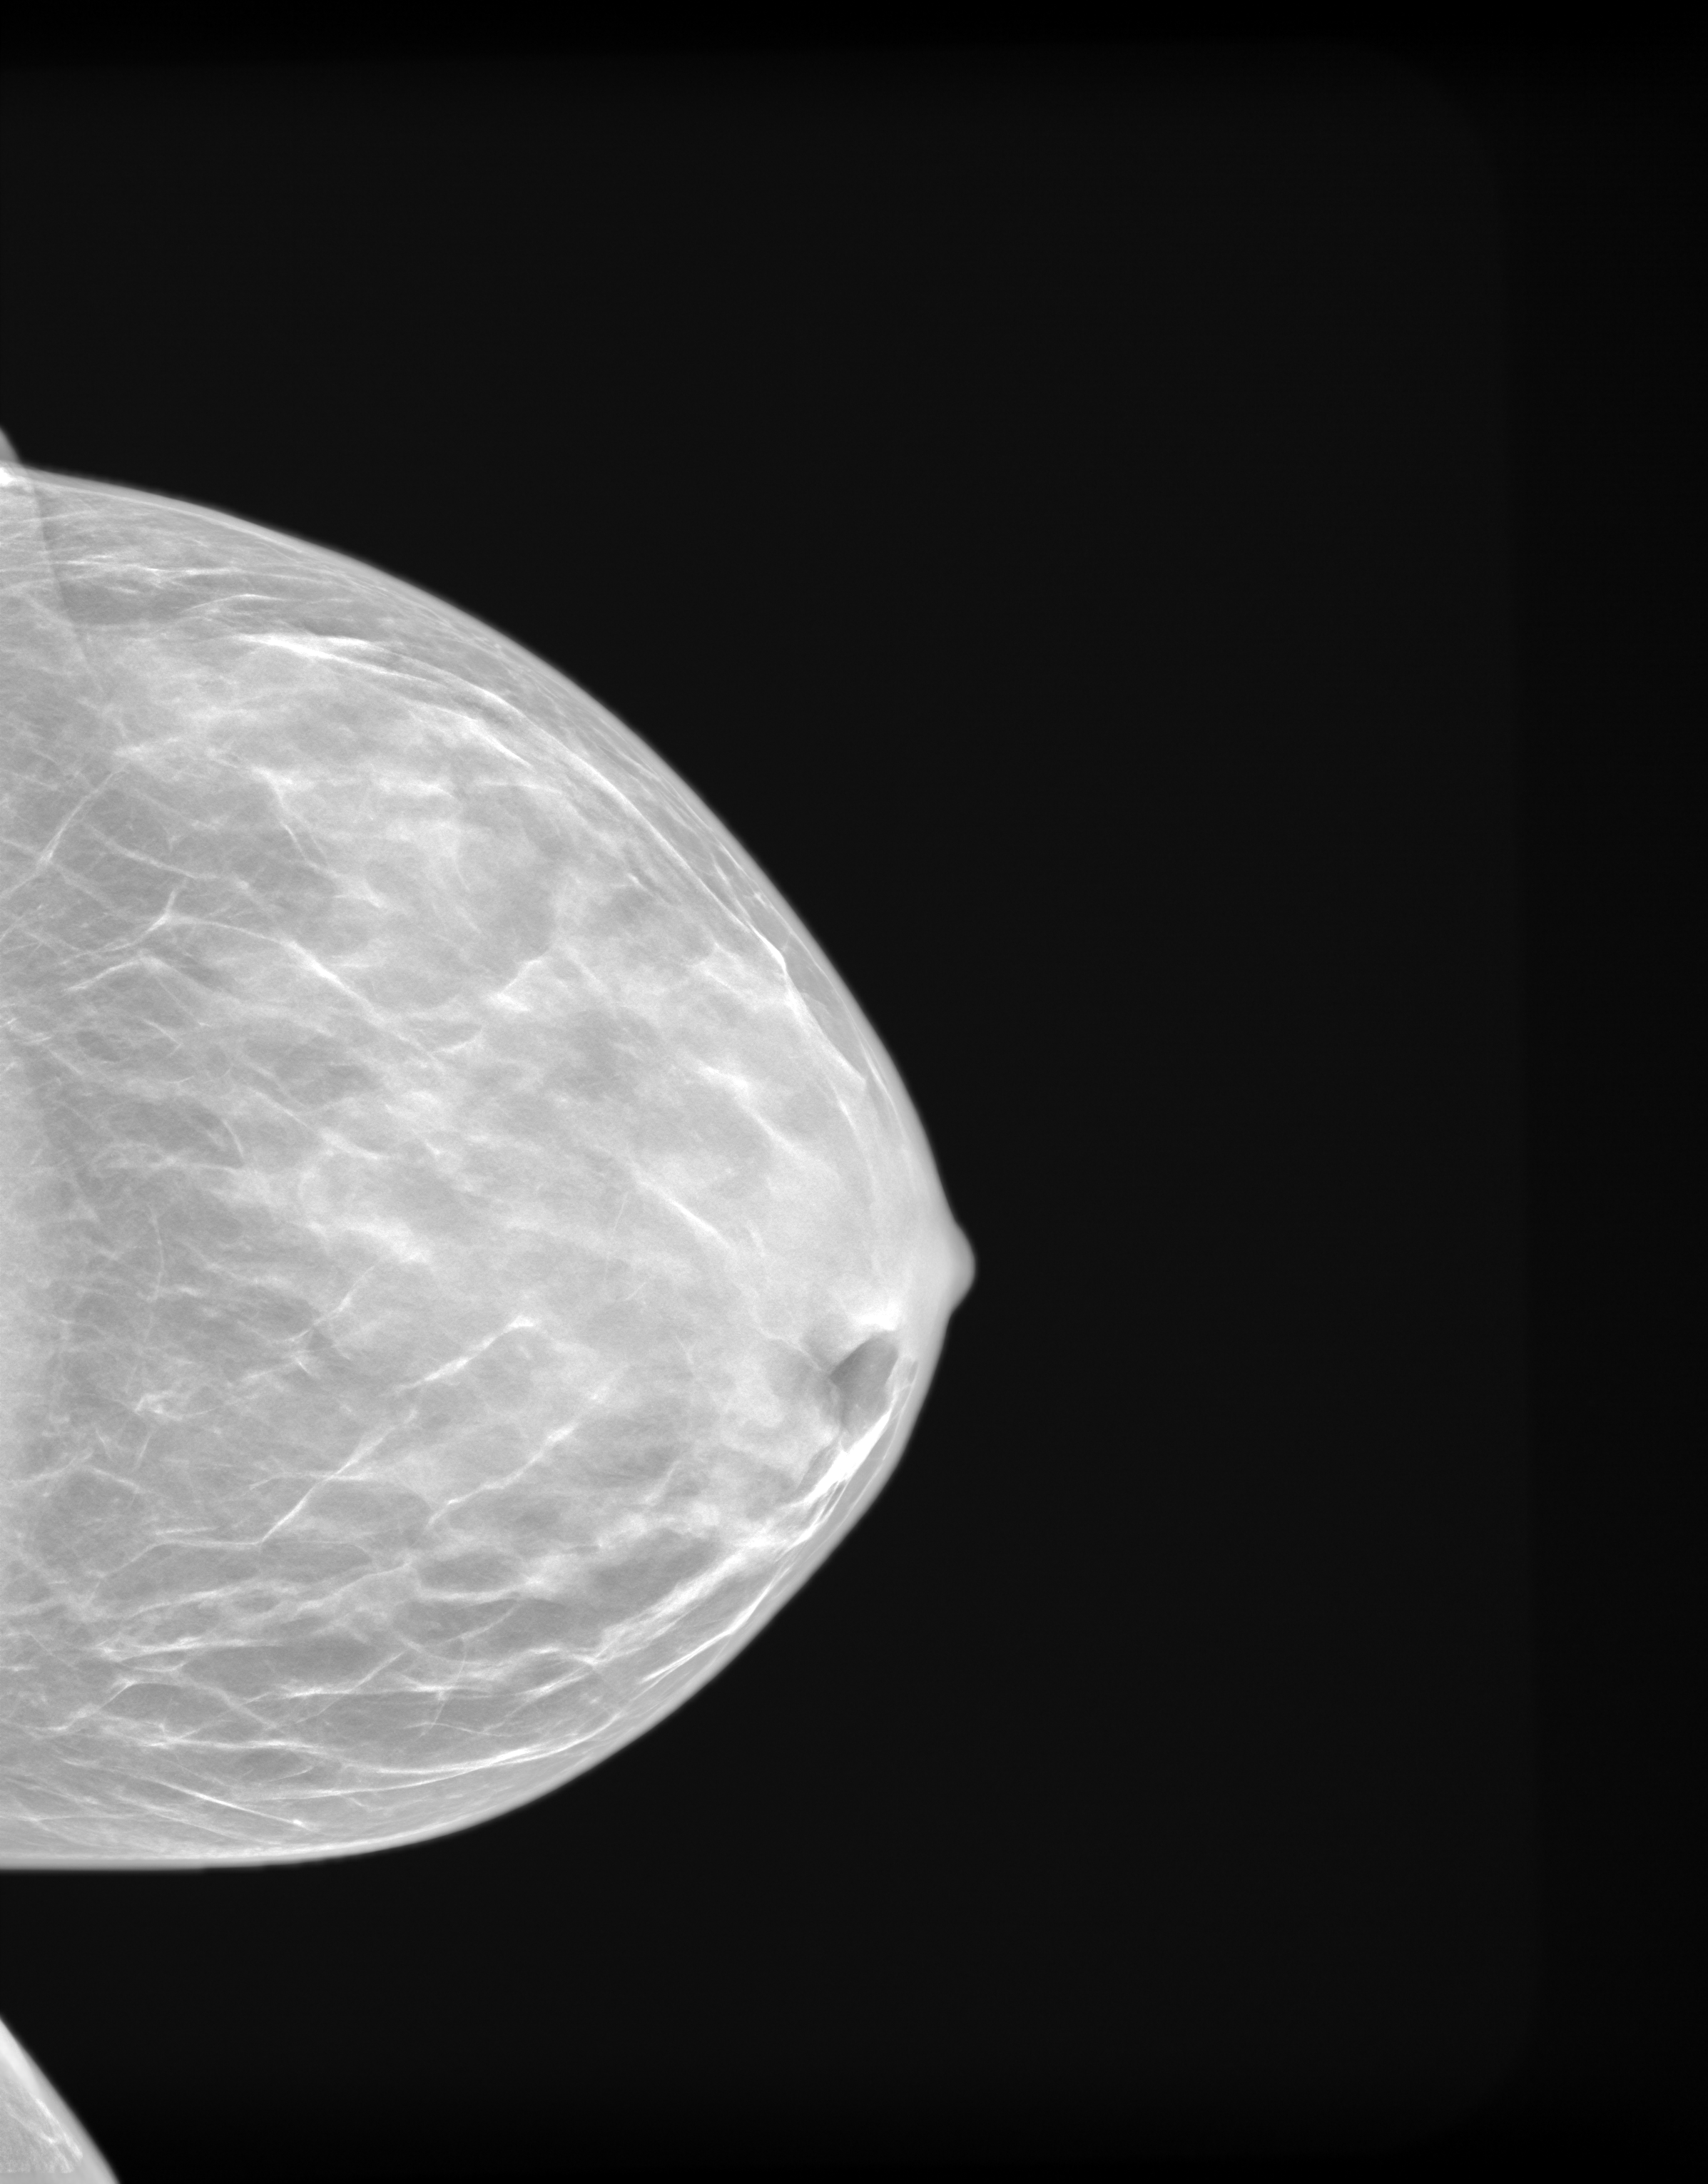
Screening examination. Patient: female, 48 years.
Image type: synthesized 2-D view from tomosynthesis. Breast: left. Projection: cranio-caudal projection.